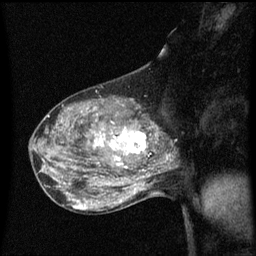
Breast MRI (dynamic contrast-enhanced), one sagittal slice. Dynamic contrast-enhanced series, image 2 of 3 at this slice position (ordered by acquisition). 1.5 T. TE 4.2 ms, TR 8.4 ms. 2 mm slice thickness. 256 × 256 image matrix, field of view 200 × 200 mm. Patient: female, 50 years.
Structures marked on this image (semi-automatic segmentation, software-assisted and operator-edited):
- analysis volume of interest (the breast-tissue region the enhancement analysis was run in; not a lesion): box from (x=100, y=114) to (x=153, y=171) px
- tumour enhancement mask (voxels above the 70 % enhancement threshold inside the analysis volume of interest): (x=100, y=128)–(x=147, y=171)